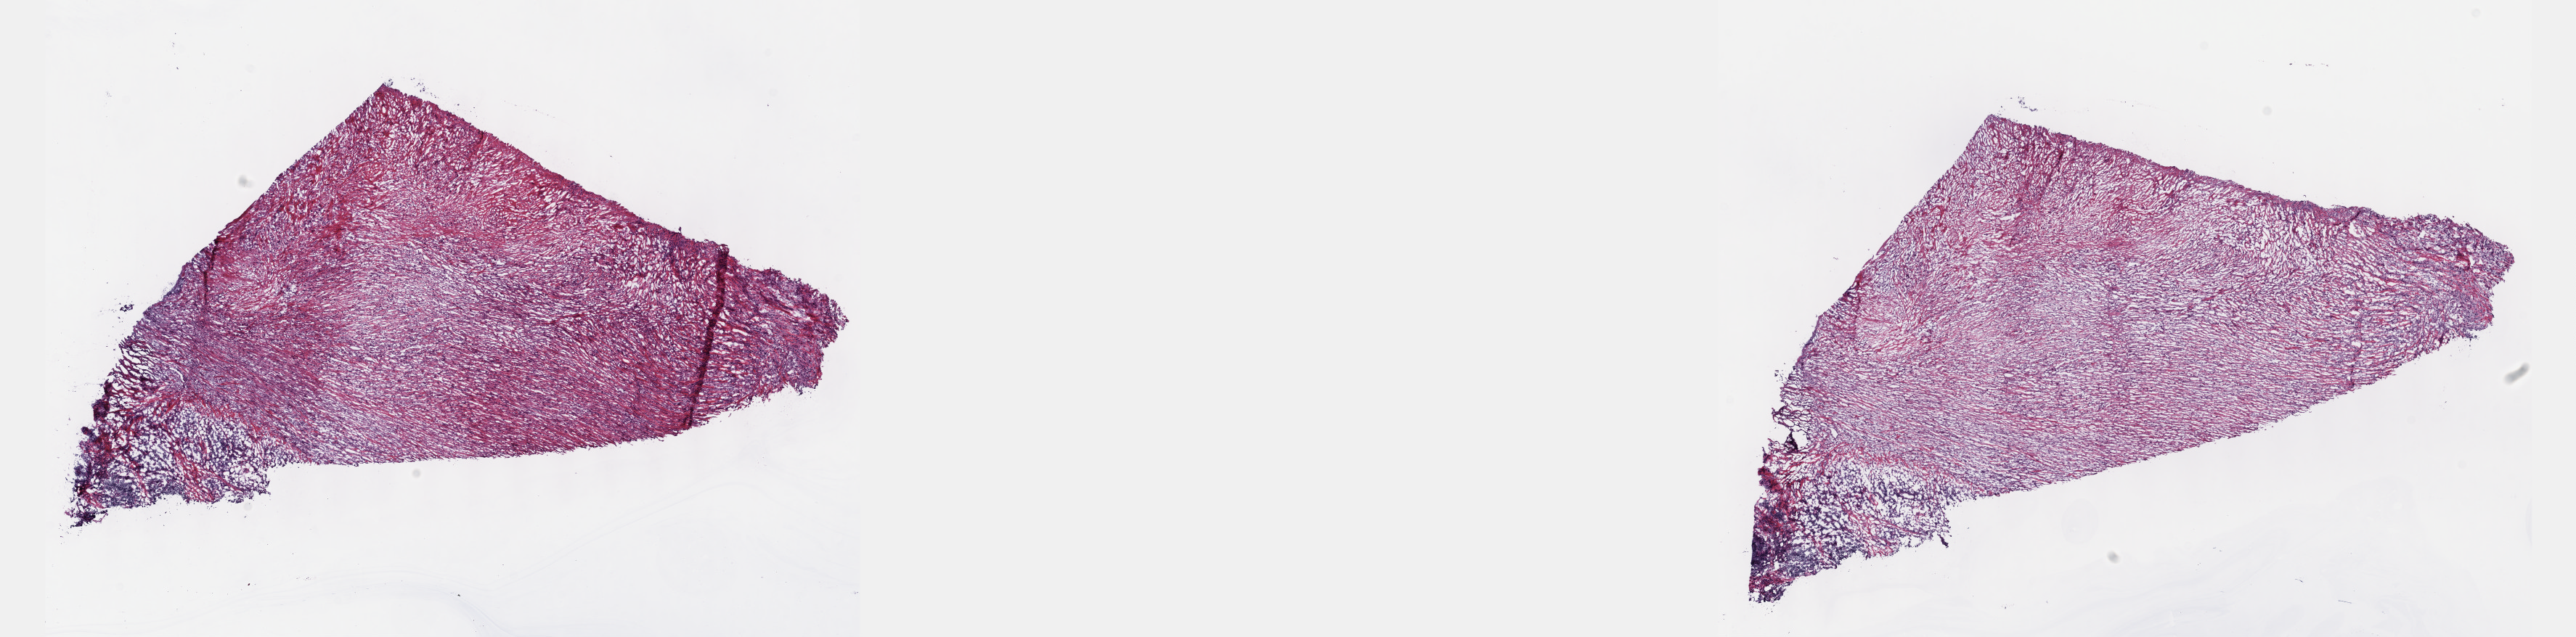
Hematoxylin and eosin (H&E) stained whole-slide image, a low-resolution overview of the entire scanned area, about 28.7 x 7.1 mm. Frozen section. Sample: primary tumour, mesothelium. Patient: male, age at initial diagnosis 60 years. Pathologist review of this section (percent, as recorded): tumour cells 27%, tumour nuclei 80%.
Pathologic diagnosis: Mesothelioma, biphasic, malignant.